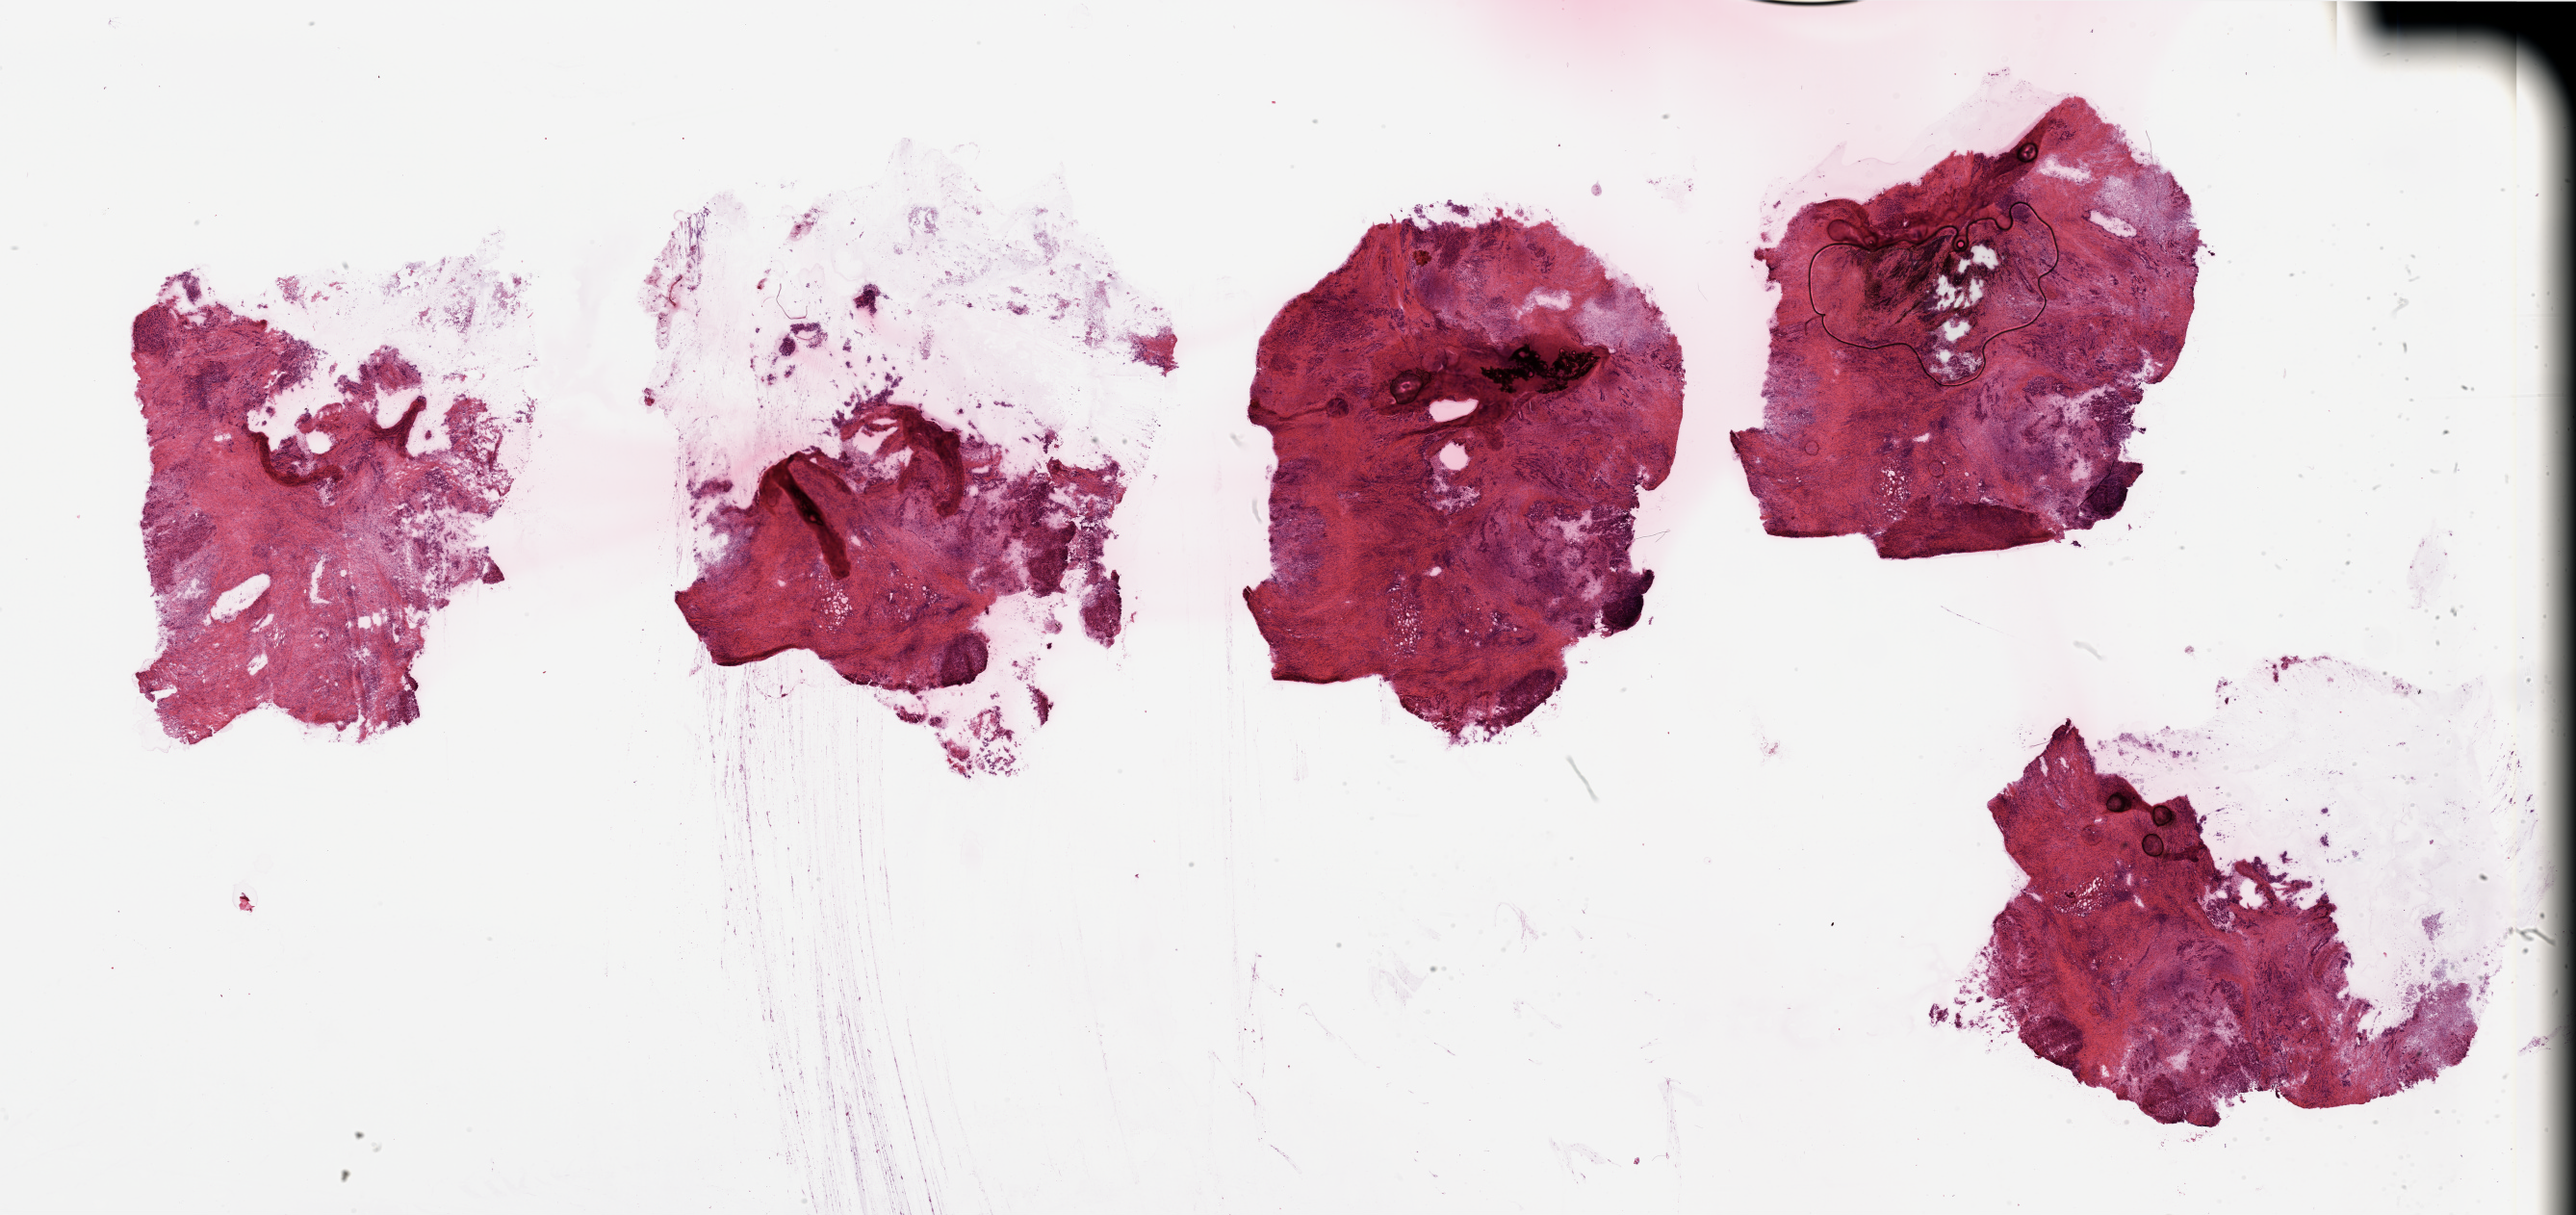
Hematoxylin and eosin (H&E) stained whole-slide image, low-resolution overview of the scanned area, about 42.3 x 20.0 mm, pancreas, tumour tissue. Male, 58 y/o.
Diagnosis: Infiltrating duct carcinoma, NOS.